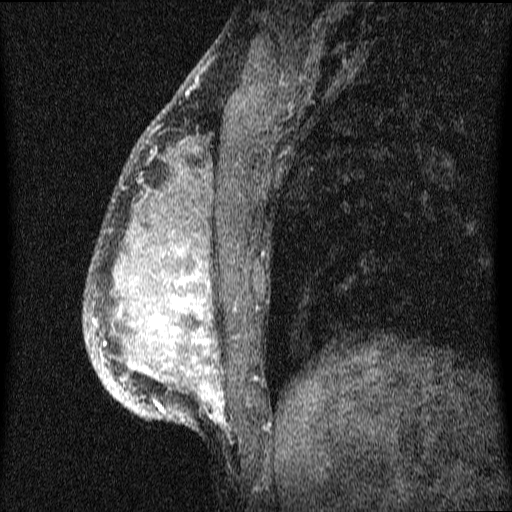
Breast MRI (dynamic contrast-enhanced), one sagittal slice; slice 22 of 64 in the series (ordered by position); dynamic contrast-enhanced series, image 2 of 4 at this slice position (ordered by acquisition); 1.5 T; TE 4.2 ms, TR 9.1 ms; 512 × 512 image matrix. Female patient, age 33 years.
Outlined on this slice (semi-automatically segmented with operator editing):
- analysis volume of interest (the breast-tissue region the enhancement analysis was run in; not a lesion): bounding box <84,151,333,458> (left, top, right, bottom; pixels)
- tumour enhancement mask (voxels above the 70 % enhancement threshold inside the analysis volume of interest): <93,249,223,422>